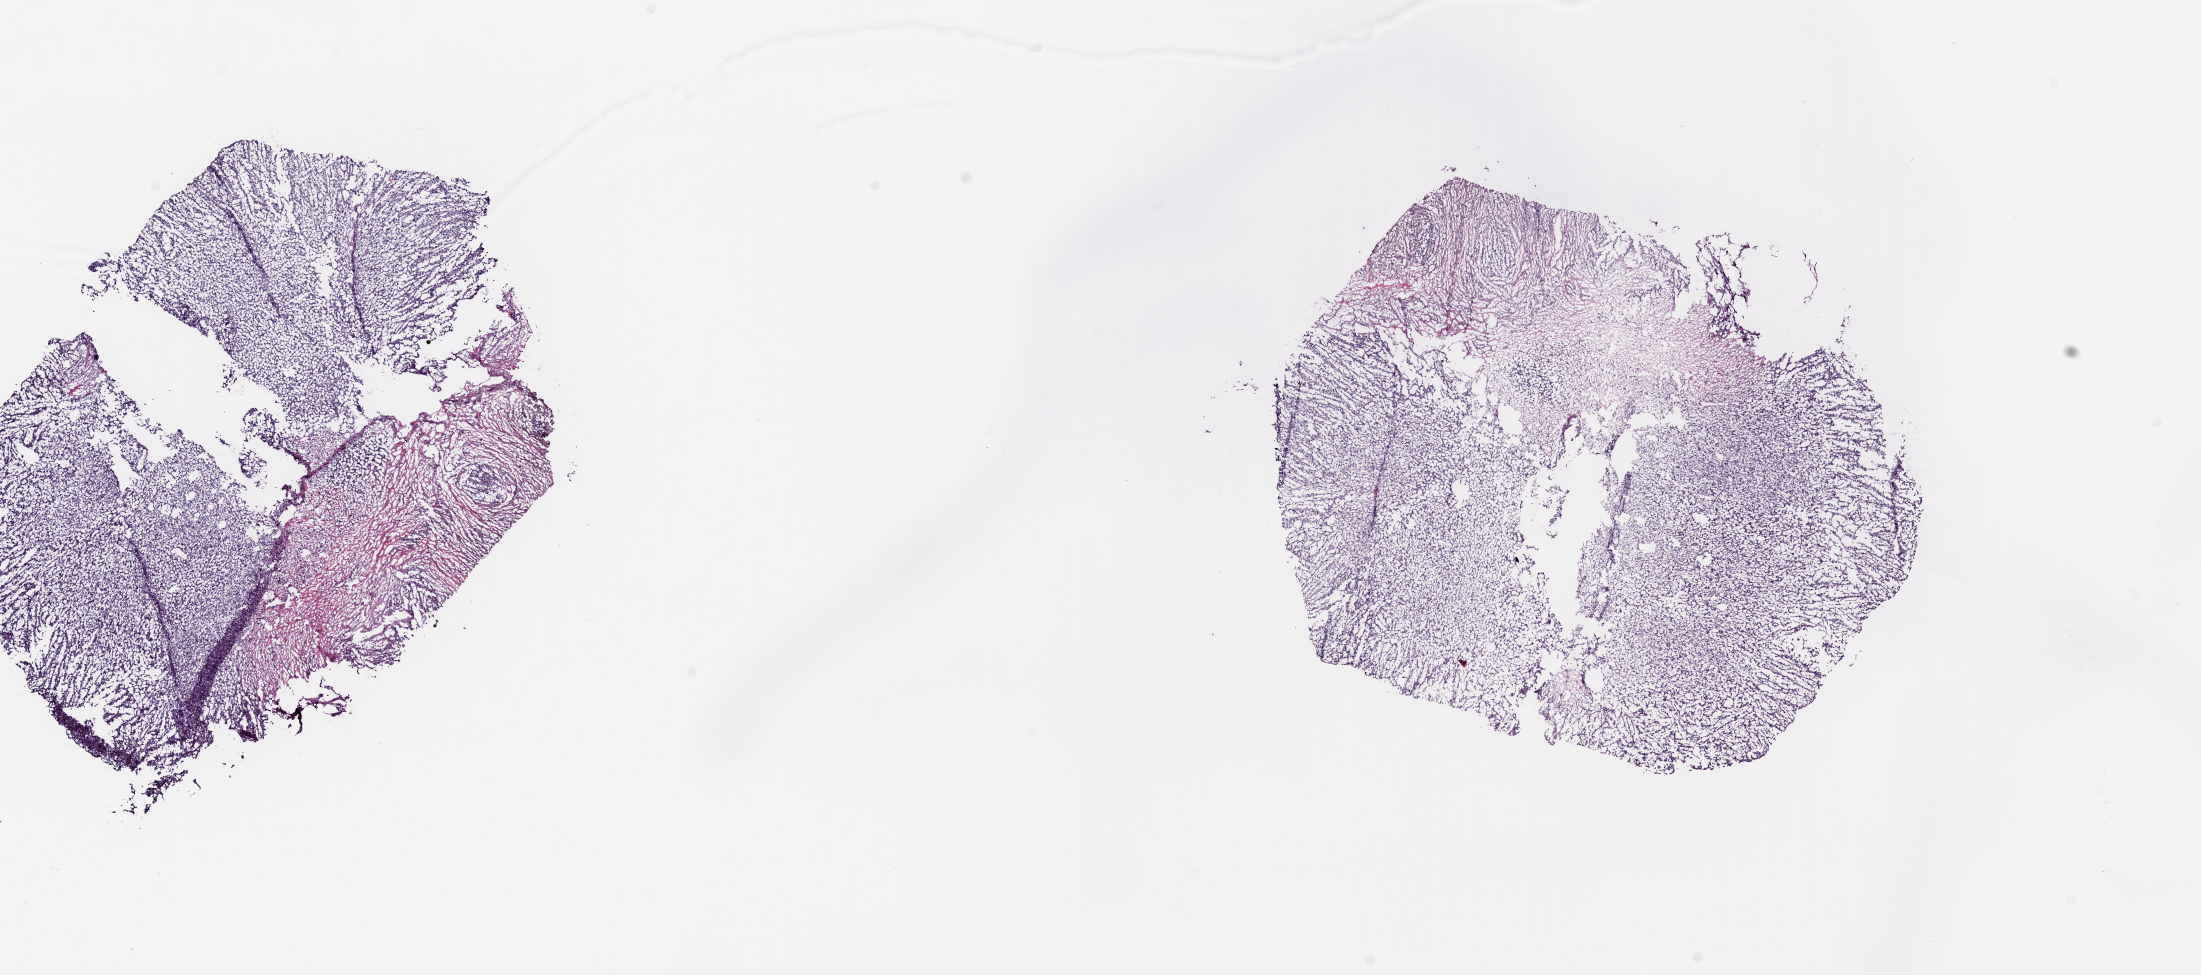
Whole-slide histology image, H&E-stained — low-resolution overview of the scanned area, about 17.4 x 7.7 mm, frozen section from the top of the tissue portion, metastatic tumour sample, sampled site: skin of lower limb and hip. Patient: female, age at initial diagnosis 66 years. Slide review estimates, as recorded: tumour cells 60%, tumour nuclei 70%, normal cells 0%, stromal cells 40%, necrosis 0%. Inflammatory infiltration, as recorded: lymphocyte infiltration 0%, monocyte infiltration 0%, neutrophil infiltration 0%.
This section: metastatic tumour tissue. Patient diagnosis: Malignant melanoma, NOS.